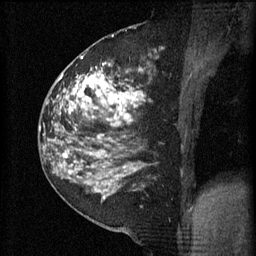
Breast MRI (dynamic contrast-enhanced), one sagittal slice; position 24 of 60 along the scan axis; 3 images stored at this slice position (order not interpretable as contrast timing); 1.5 T; TE 4.2 ms, TR 11 ms; 256 × 256 image matrix, field of view 180 × 180 mm. Female patient, age 52 years.
Annotated regions visible in this slice (semi-automatic segmentation, software-assisted and operator-edited):
- analysis volume of interest (the breast-tissue region the enhancement analysis was run in; not a lesion): box from (x=81, y=54) to (x=151, y=157) px
- tumour enhancement mask (voxels above the 70 % enhancement threshold inside the analysis volume of interest): (x=81, y=58)–(x=145, y=157)